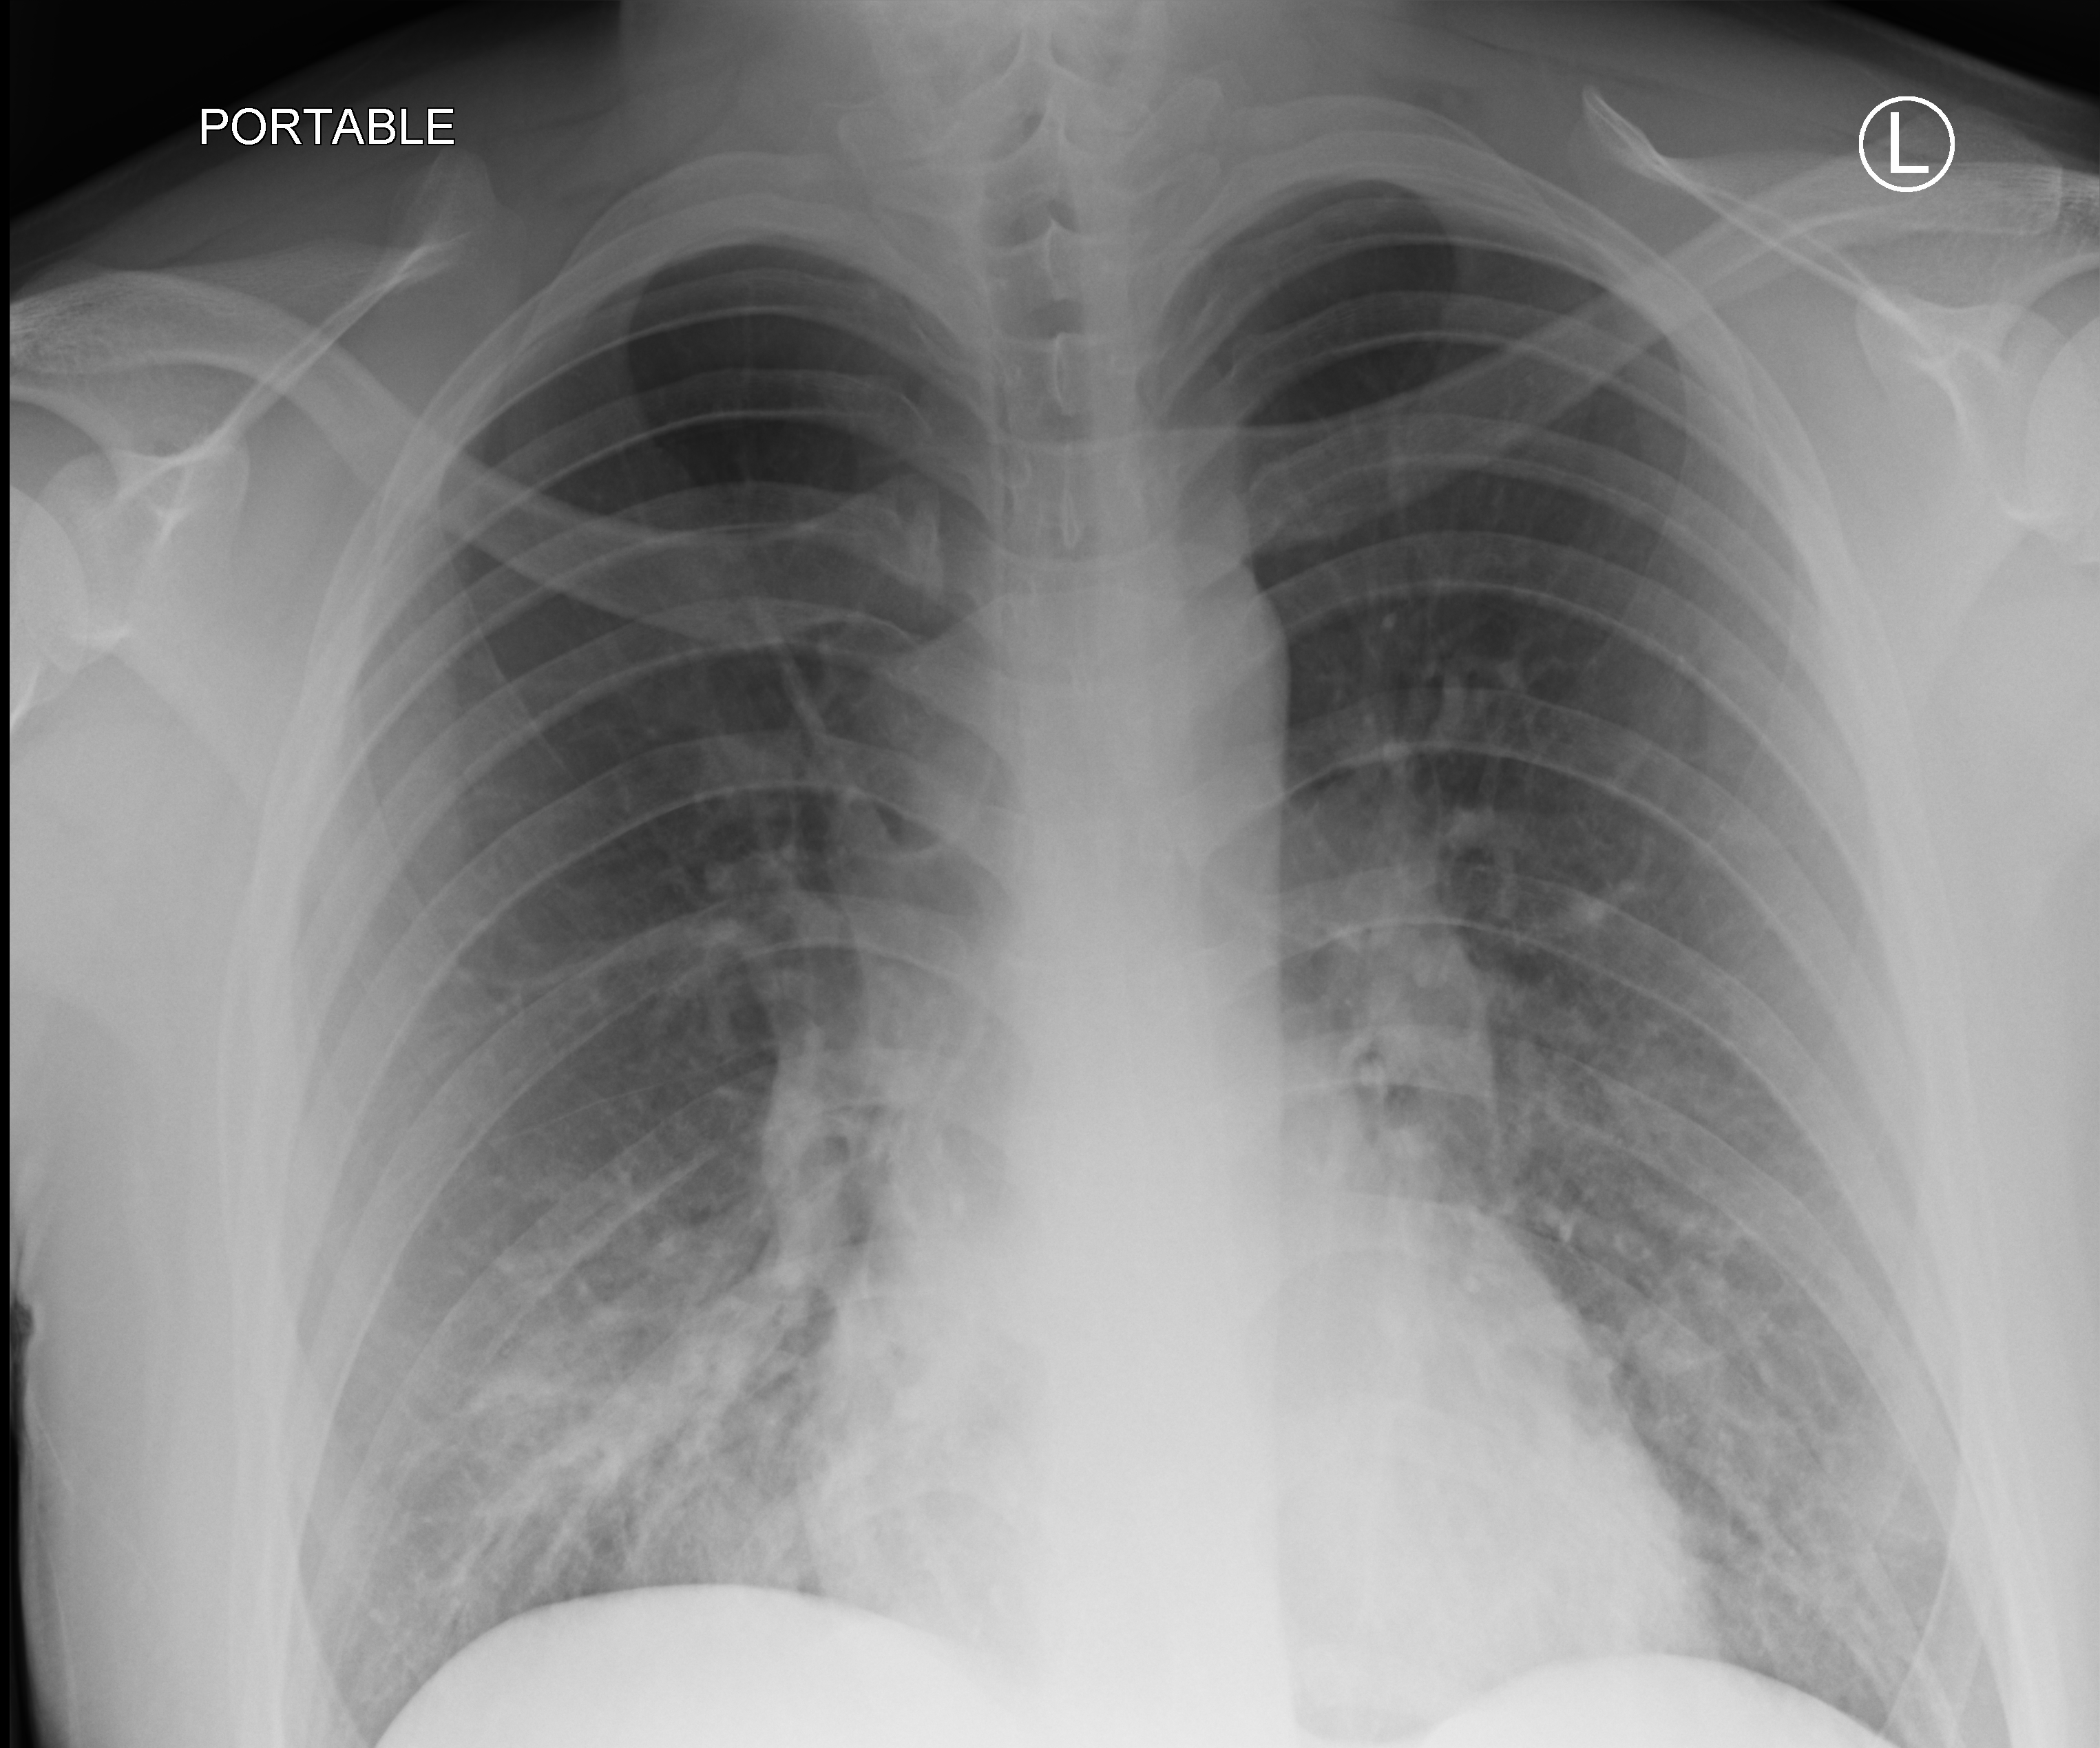
Chest X-ray (portable); anteroposterior (AP) projection. Male patient hospitalised with COVID-19, age 18–59 years.
Hospital-stay facts (about this admission, not read from this image; timing relative to this image not recorded): other chronic lung disease (admission record): no; mechanically ventilated during this hospital stay: no.